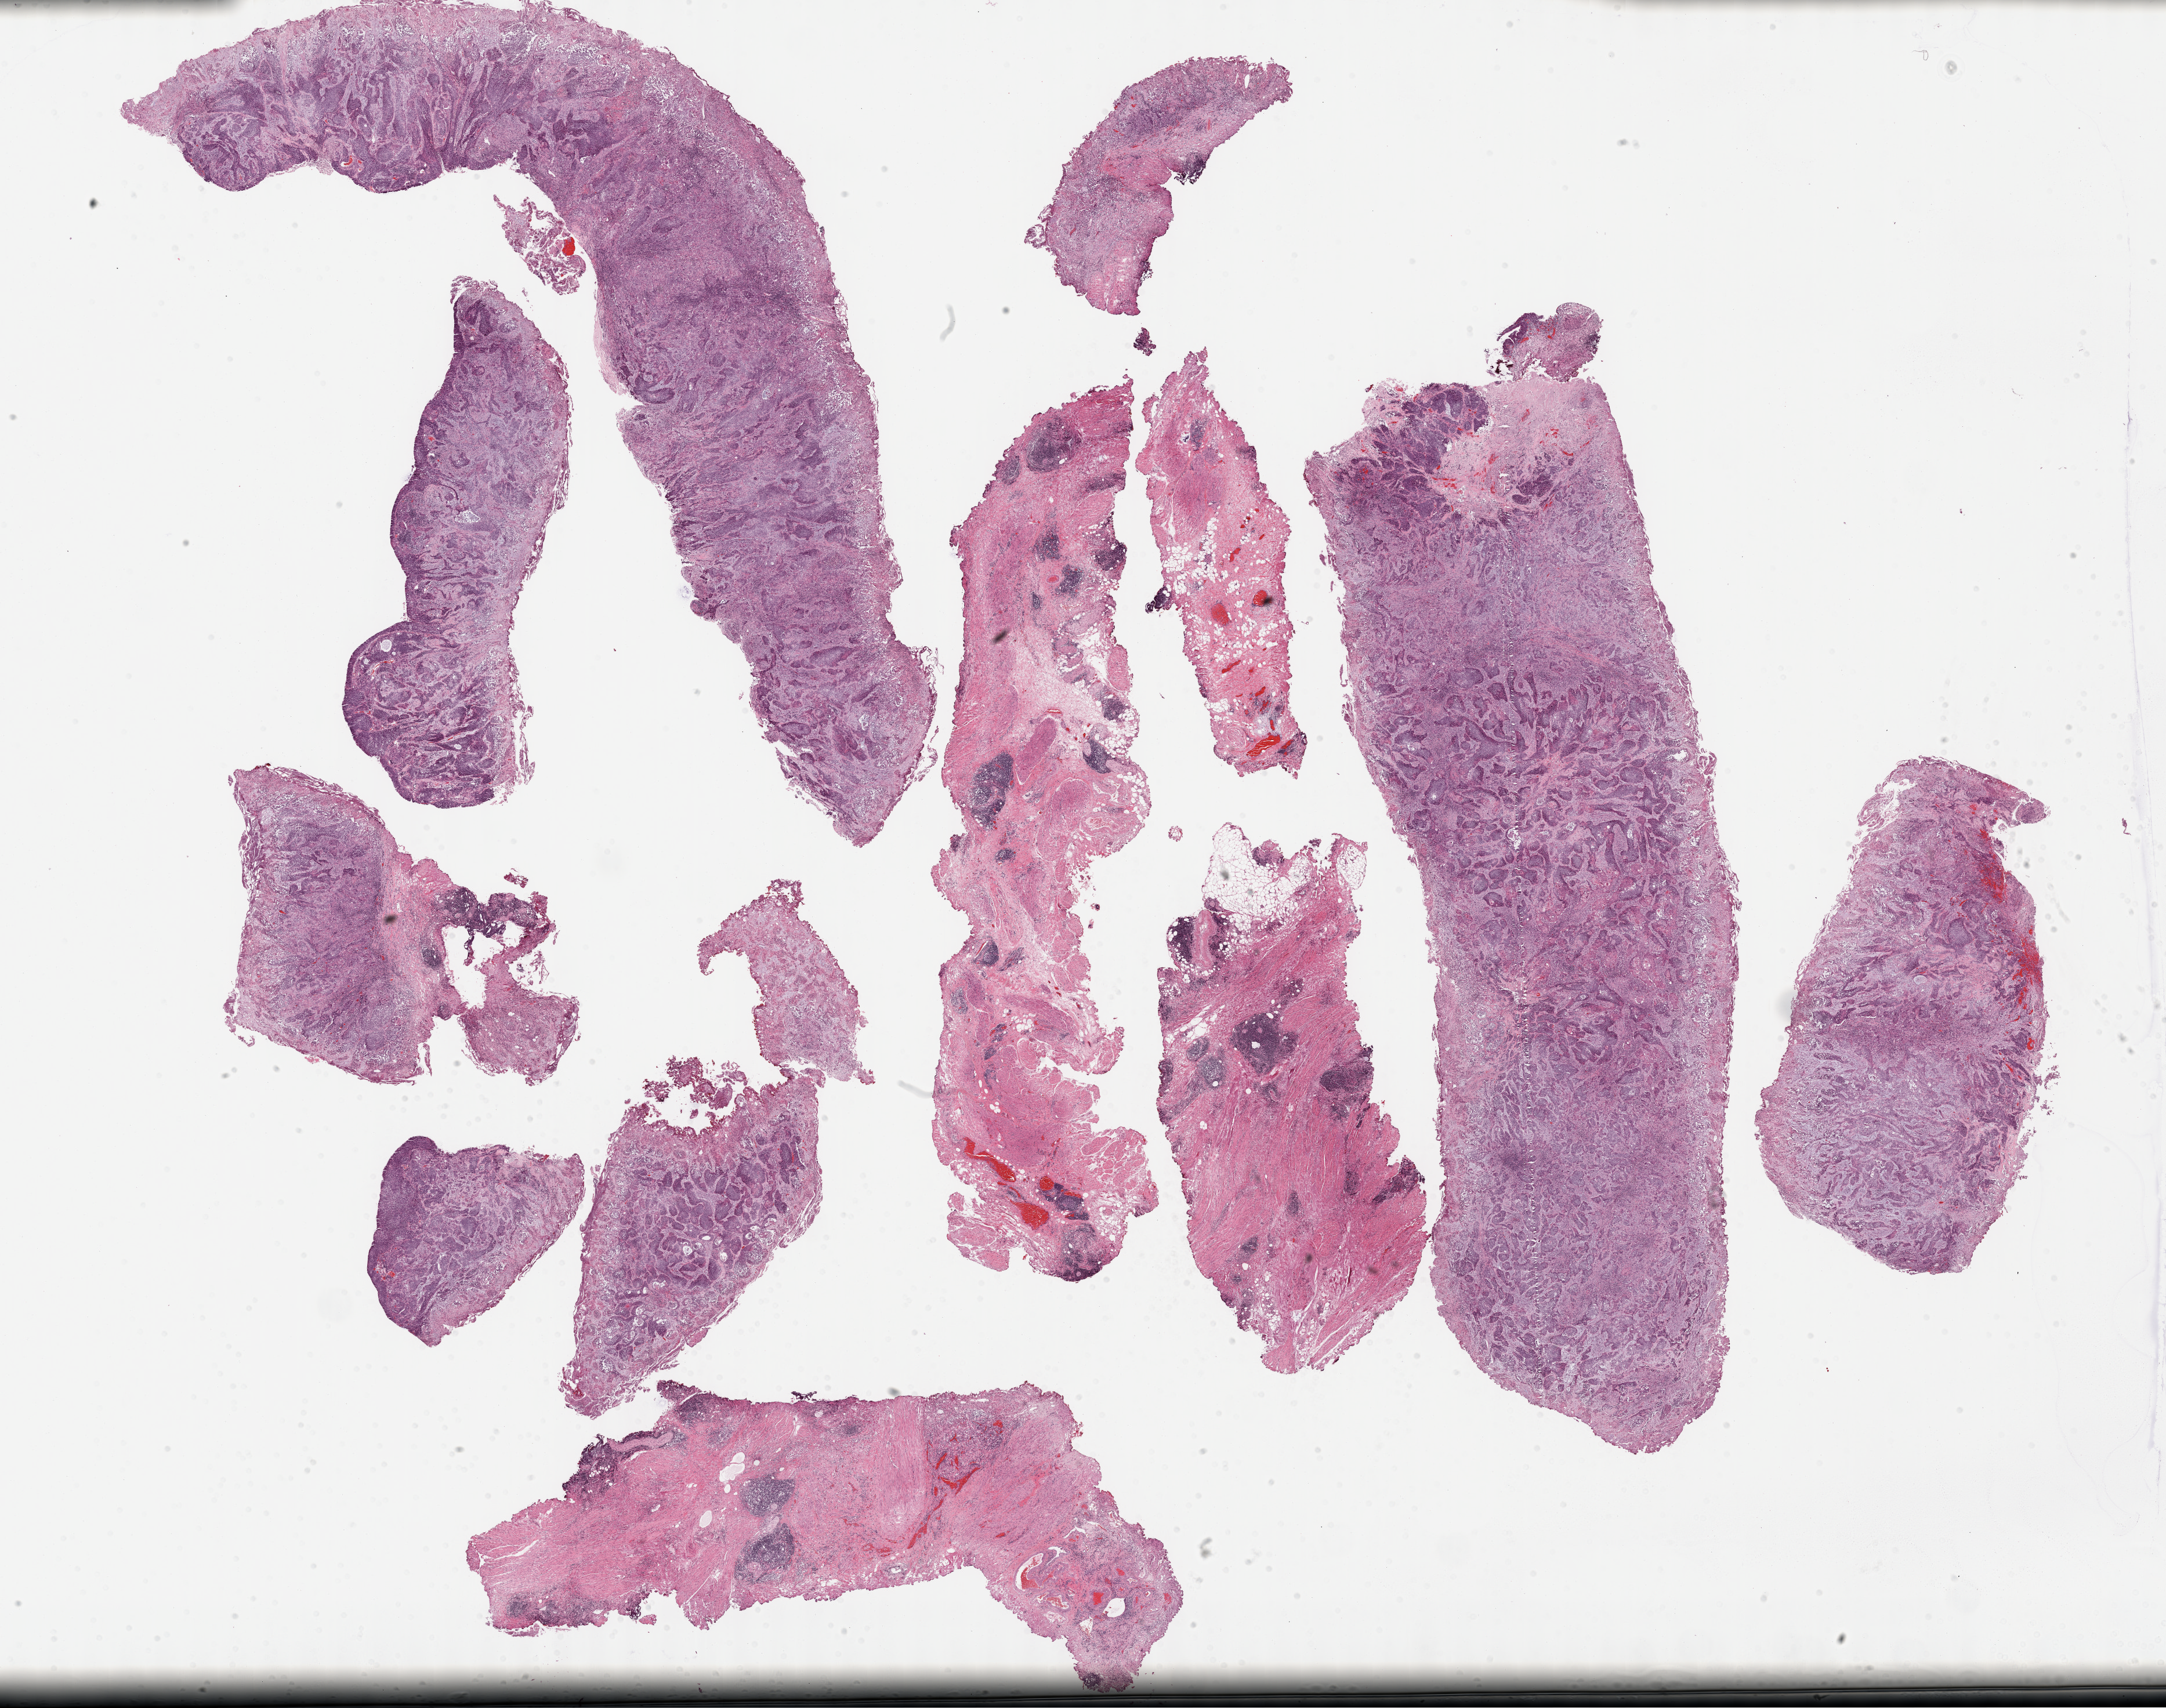
Whole-slide histology image, H&E — a low-resolution overview of the entire scanned area, about 30.2 x 23.8 mm (slide scanned at 40x), formalin-fixed paraffin-embedded (FFPE) diagnostic section, bladder, primary tumour sample. Female patient; age at initial diagnosis 78 years. Histologic grade: high grade.
AJCC pathologic stage: II (7th edition). Pathologic diagnosis: Transitional cell carcinoma.